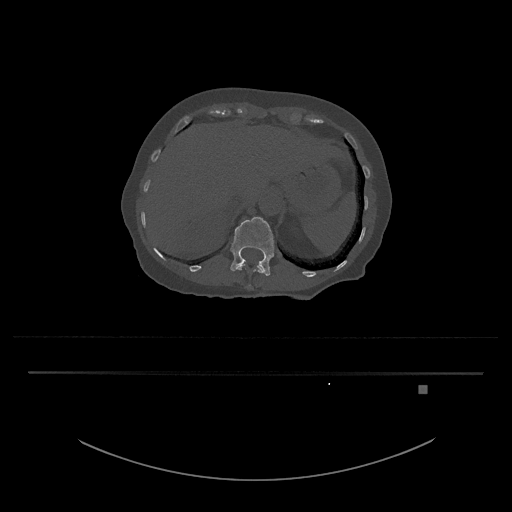
CT including the spine, one axial slice. Slice 575 of 797 in the series (ordered by position). Reconstruction kernel Br40s/3. 120 kVp. Bone window (W 1800 / L 400 HU). 0.5 mm slice thickness. 512 × 512 image matrix, field of view 500 × 500 mm. Patient: female, 57 years. From the clinical record (not read from this slice): primary cancer: cervical.
Annotated regions visible in this slice (semi-automatically segmented with operator editing):
- L1 vertebra: bounding box [x1, y1, x2, y2] px = [230, 217, 274, 276]
- T12 vertebra: [236, 263, 265, 286]